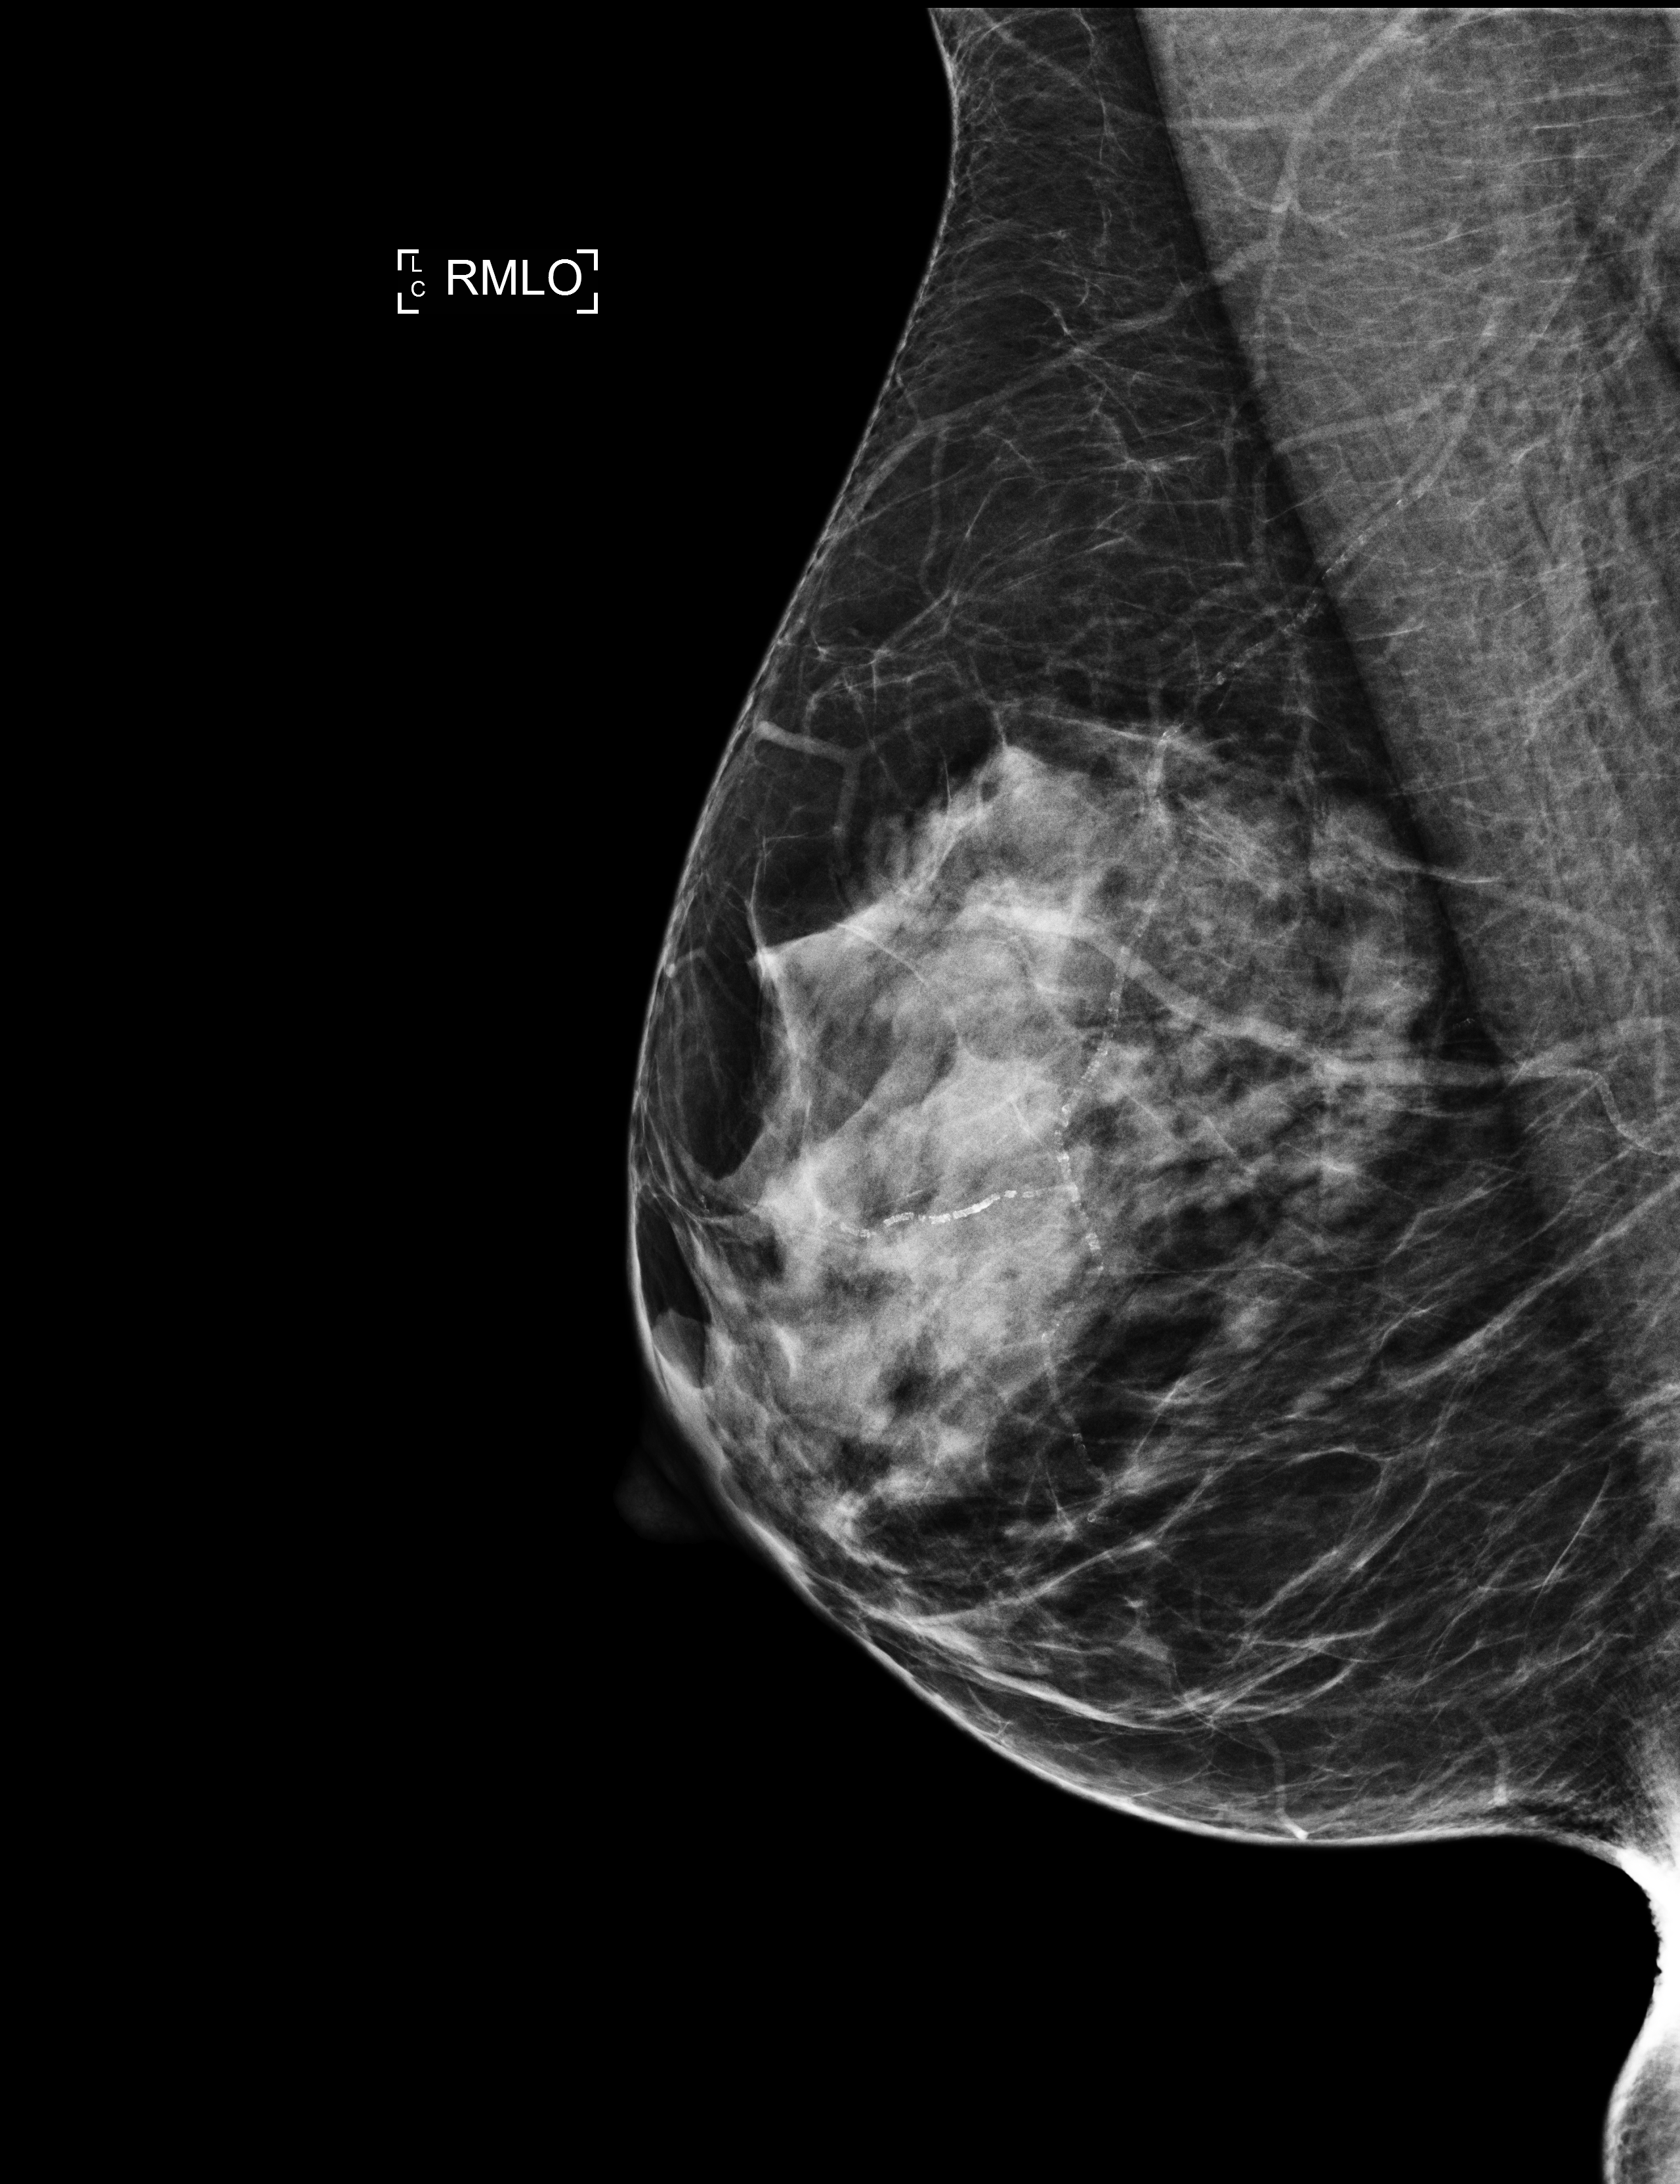
Digital mammogram (FFDM); right breast; MLO view; screening examination. Patient aged 57 years (female).
- BI-RADS breast density category at the screening exam (both breasts, scale 1–4): 3
- final BI-RADS category for the screening round (tomosynthesis exam, both breasts): category 1
- recall: no recall after this screen